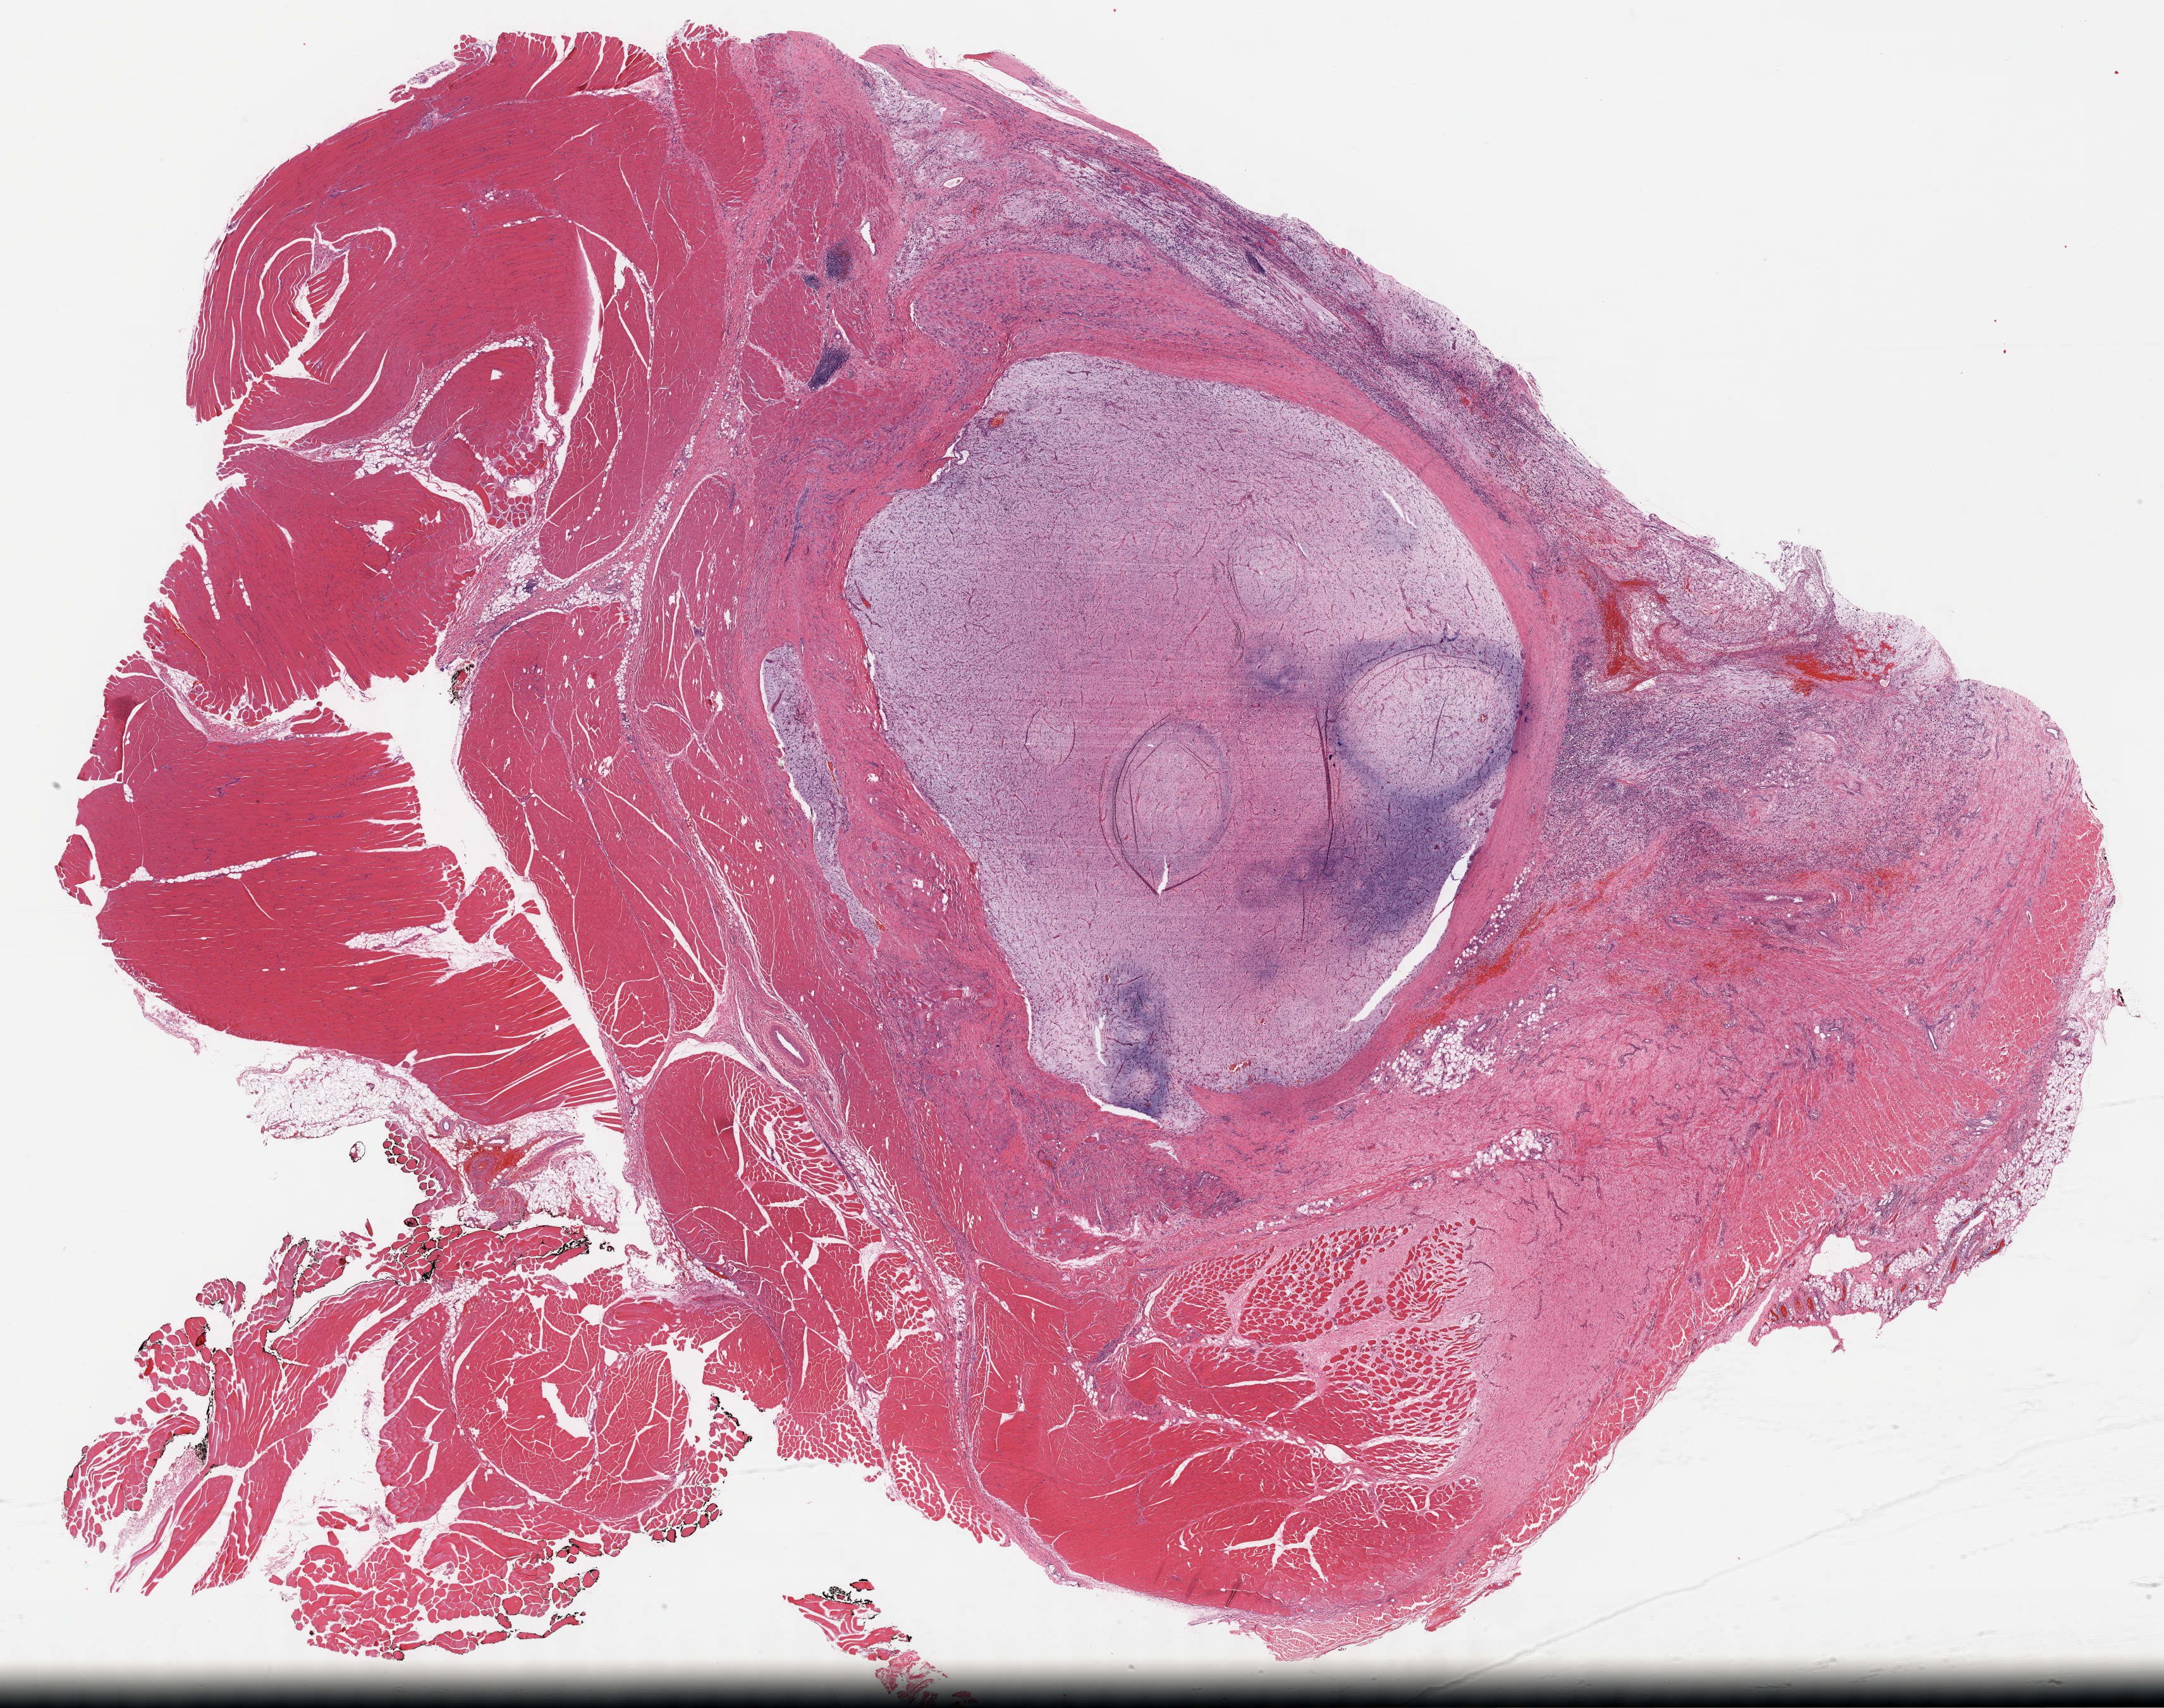
Digitized H&E-stained tissue section (whole slide) — a low-resolution overview of the entire scanned area, about 27.7 x 21.9 mm (from a 40x scan). Formalin-fixed paraffin-embedded (FFPE) diagnostic section. Sample: primary tumour, connective, subcutaneous and other soft tissues. Patient: male, age at initial diagnosis 35 years.
Diagnosis: Fibromyxosarcoma (connective, subcutaneous and other soft tissues of lower limb and hip).